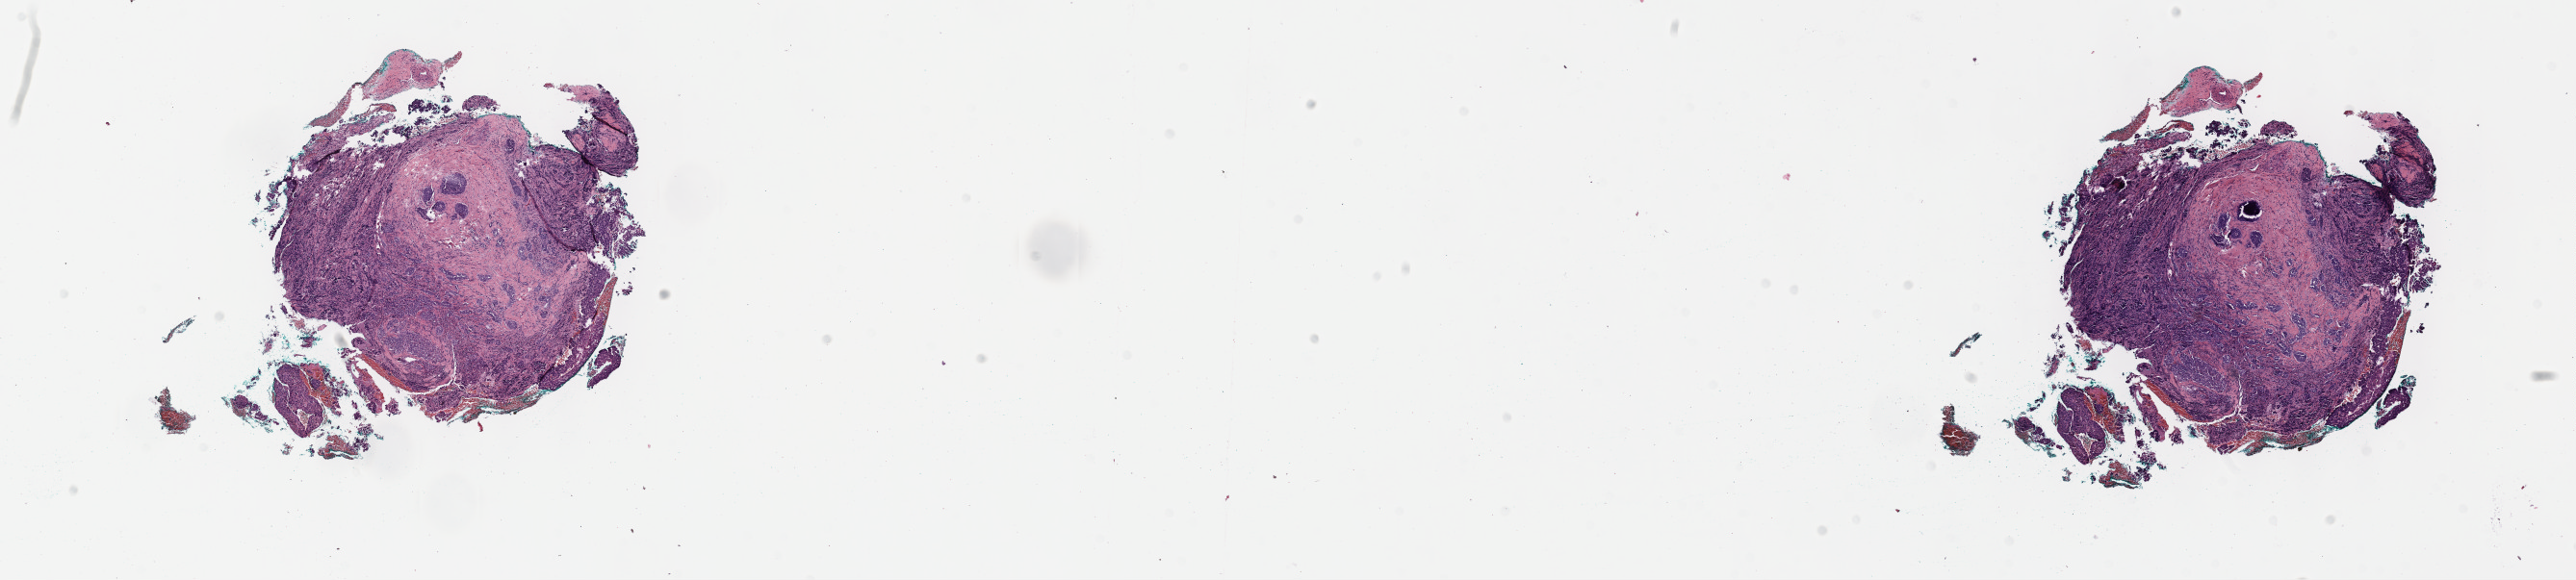
Hematoxylin and eosin (H&E) stained whole-slide image, shown as a low-resolution overview of the whole scanned area (about 21.6 x 4.9 mm, from a 40x scan), formalin-fixed paraffin-embedded (FFPE) diagnostic section, primary tumour sample from the cervix. Female patient; age at initial diagnosis 76 years. Histologic grade: G3 (poorly differentiated).
- diagnosis: Squamous cell carcinoma, NOS (cervix uteri)
- FIGO stage: IIB